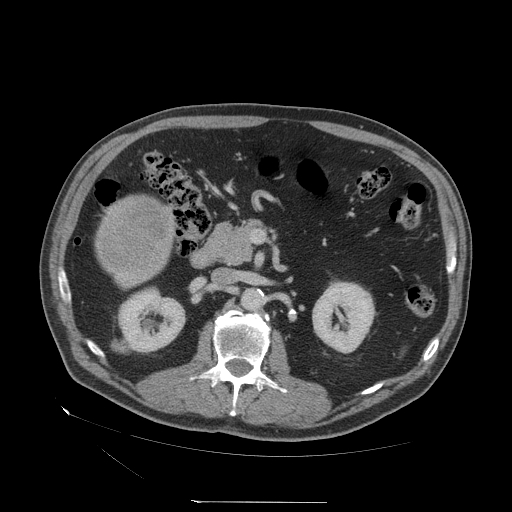
Contrast-enhanced abdominal CT (liver protocol), one axial slice; position 9 of 83 along the scan axis; reconstruction kernel STANDARD; soft-tissue window (W 400 / L 40 HU); 2.5 mm slice thickness; 512 × 512 image matrix, field of view 460 × 460 mm. Case-level facts recorded for this patient, not image findings: diagnosis: hepatocellular carcinoma (patient treated with transarterial chemoembolisation; whether this scan precedes or follows treatment is not stated here); TNM stage (as recorded): Stage-I; Child-Pugh class: A; tumour nodularity: uninodular.
Annotated regions visible in this slice (semi-automatic segmentation, software-assisted and operator-edited):
- mass: bounding box [x1, y1, x2, y2] px = [96, 195, 176, 274]